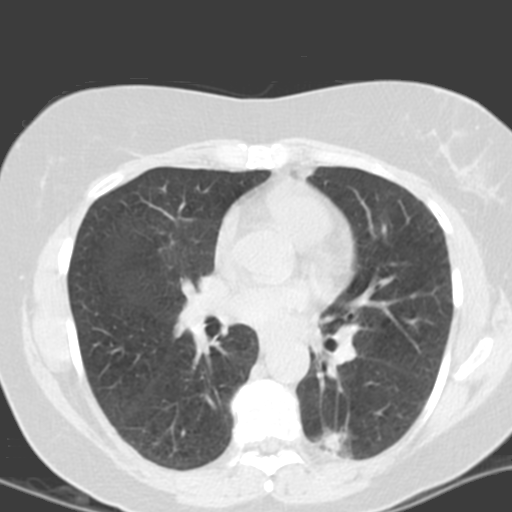
Low-dose screening chest CT, axial slice. Second annual screen. Lung window (W 1500 / L -600 HU). 3.2 mm slice thickness. 512 × 512 image matrix, field of view 290 × 290 mm. Female, age 55 years at enrolment. Current smoker at enrolment.
Expert-annotated lung lesion, bounding box <305,410,380,469> (left, top, right, bottom; pixels). The screening reader recorded 4 non-calcified nodules or masses ≥4 mm on this exam (left lower lobe, left lower lobe, left upper lobe, right middle lobe); which of them this box marks is not recorded. Lung cancer was diagnosed 688 days after this screen: adenocarcinoma with mixed subtypes, left lower lobe, poorly differentiated (G3), stage IA (AJCC 6th edition), 21 mm at pathology.